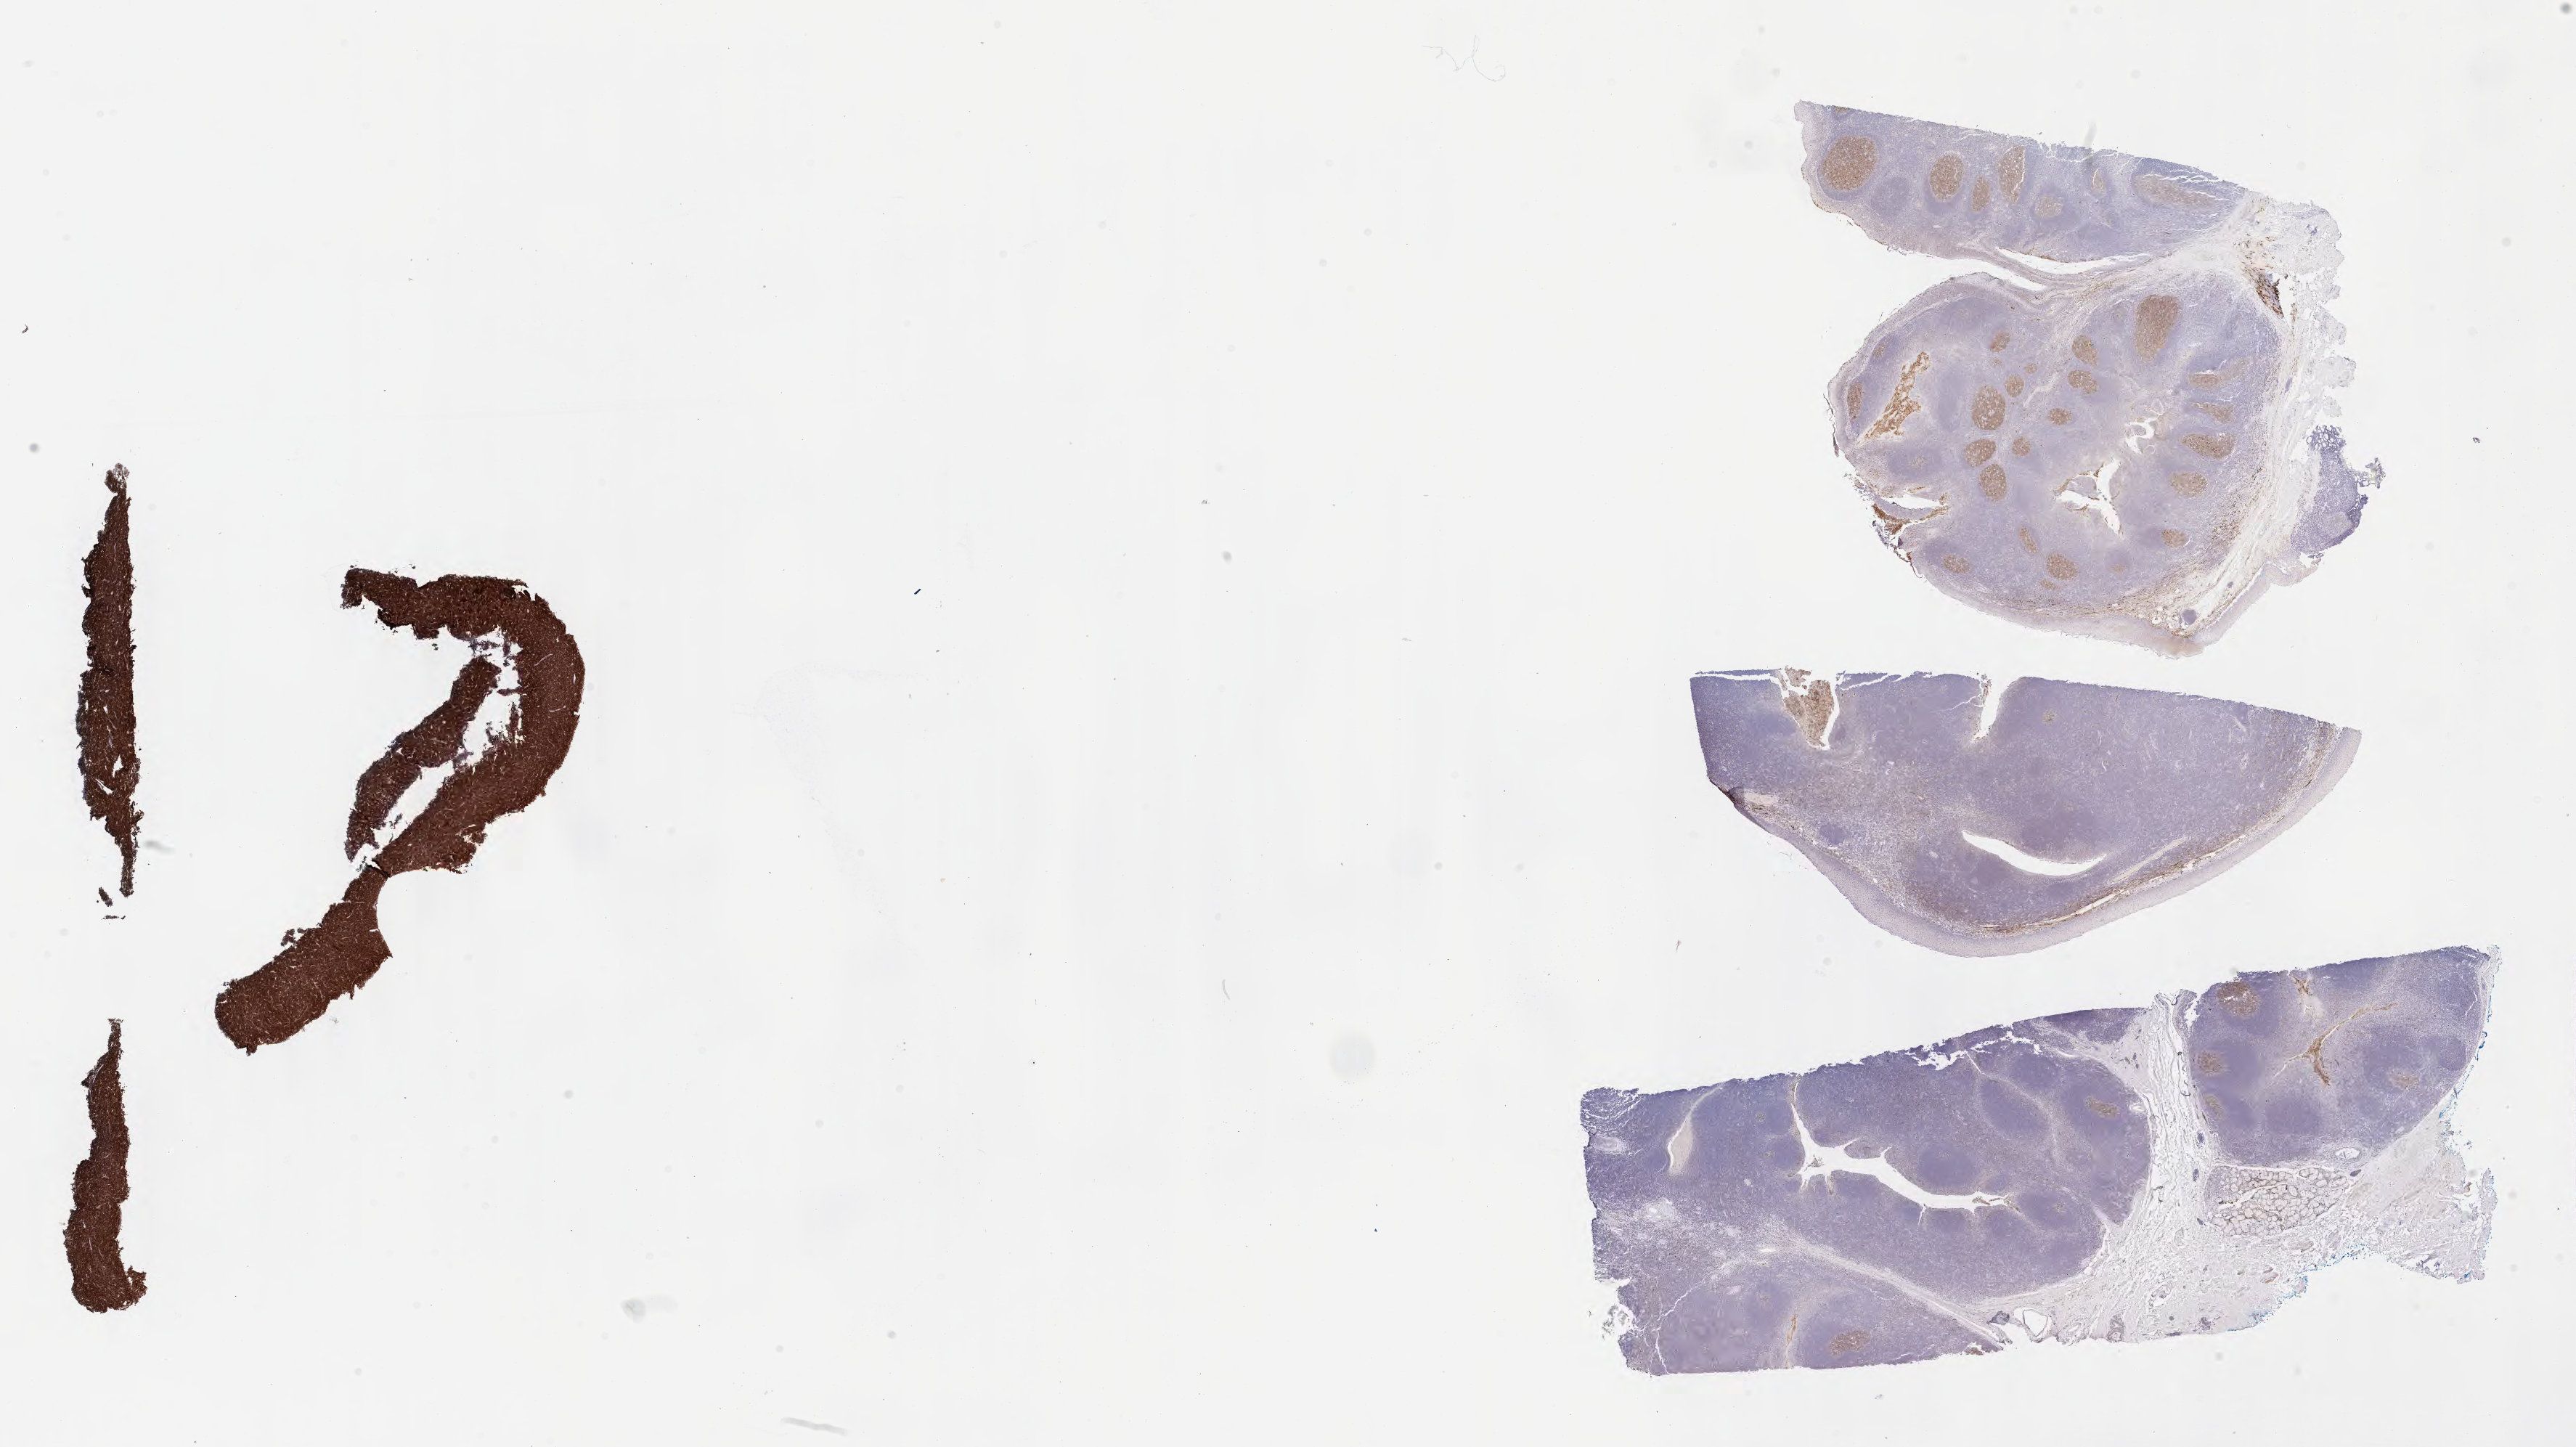
Immunohistochemistry (IHC) whole-slide image stained for CD10, low-resolution overview of the scanned area, about 28.7 x 16.1 mm. Tumor tissue. Anatomic site: peritoneum. Female, age 7 years at initial diagnosis.
Diagnosis: Burkitt lymphoma, NOS.